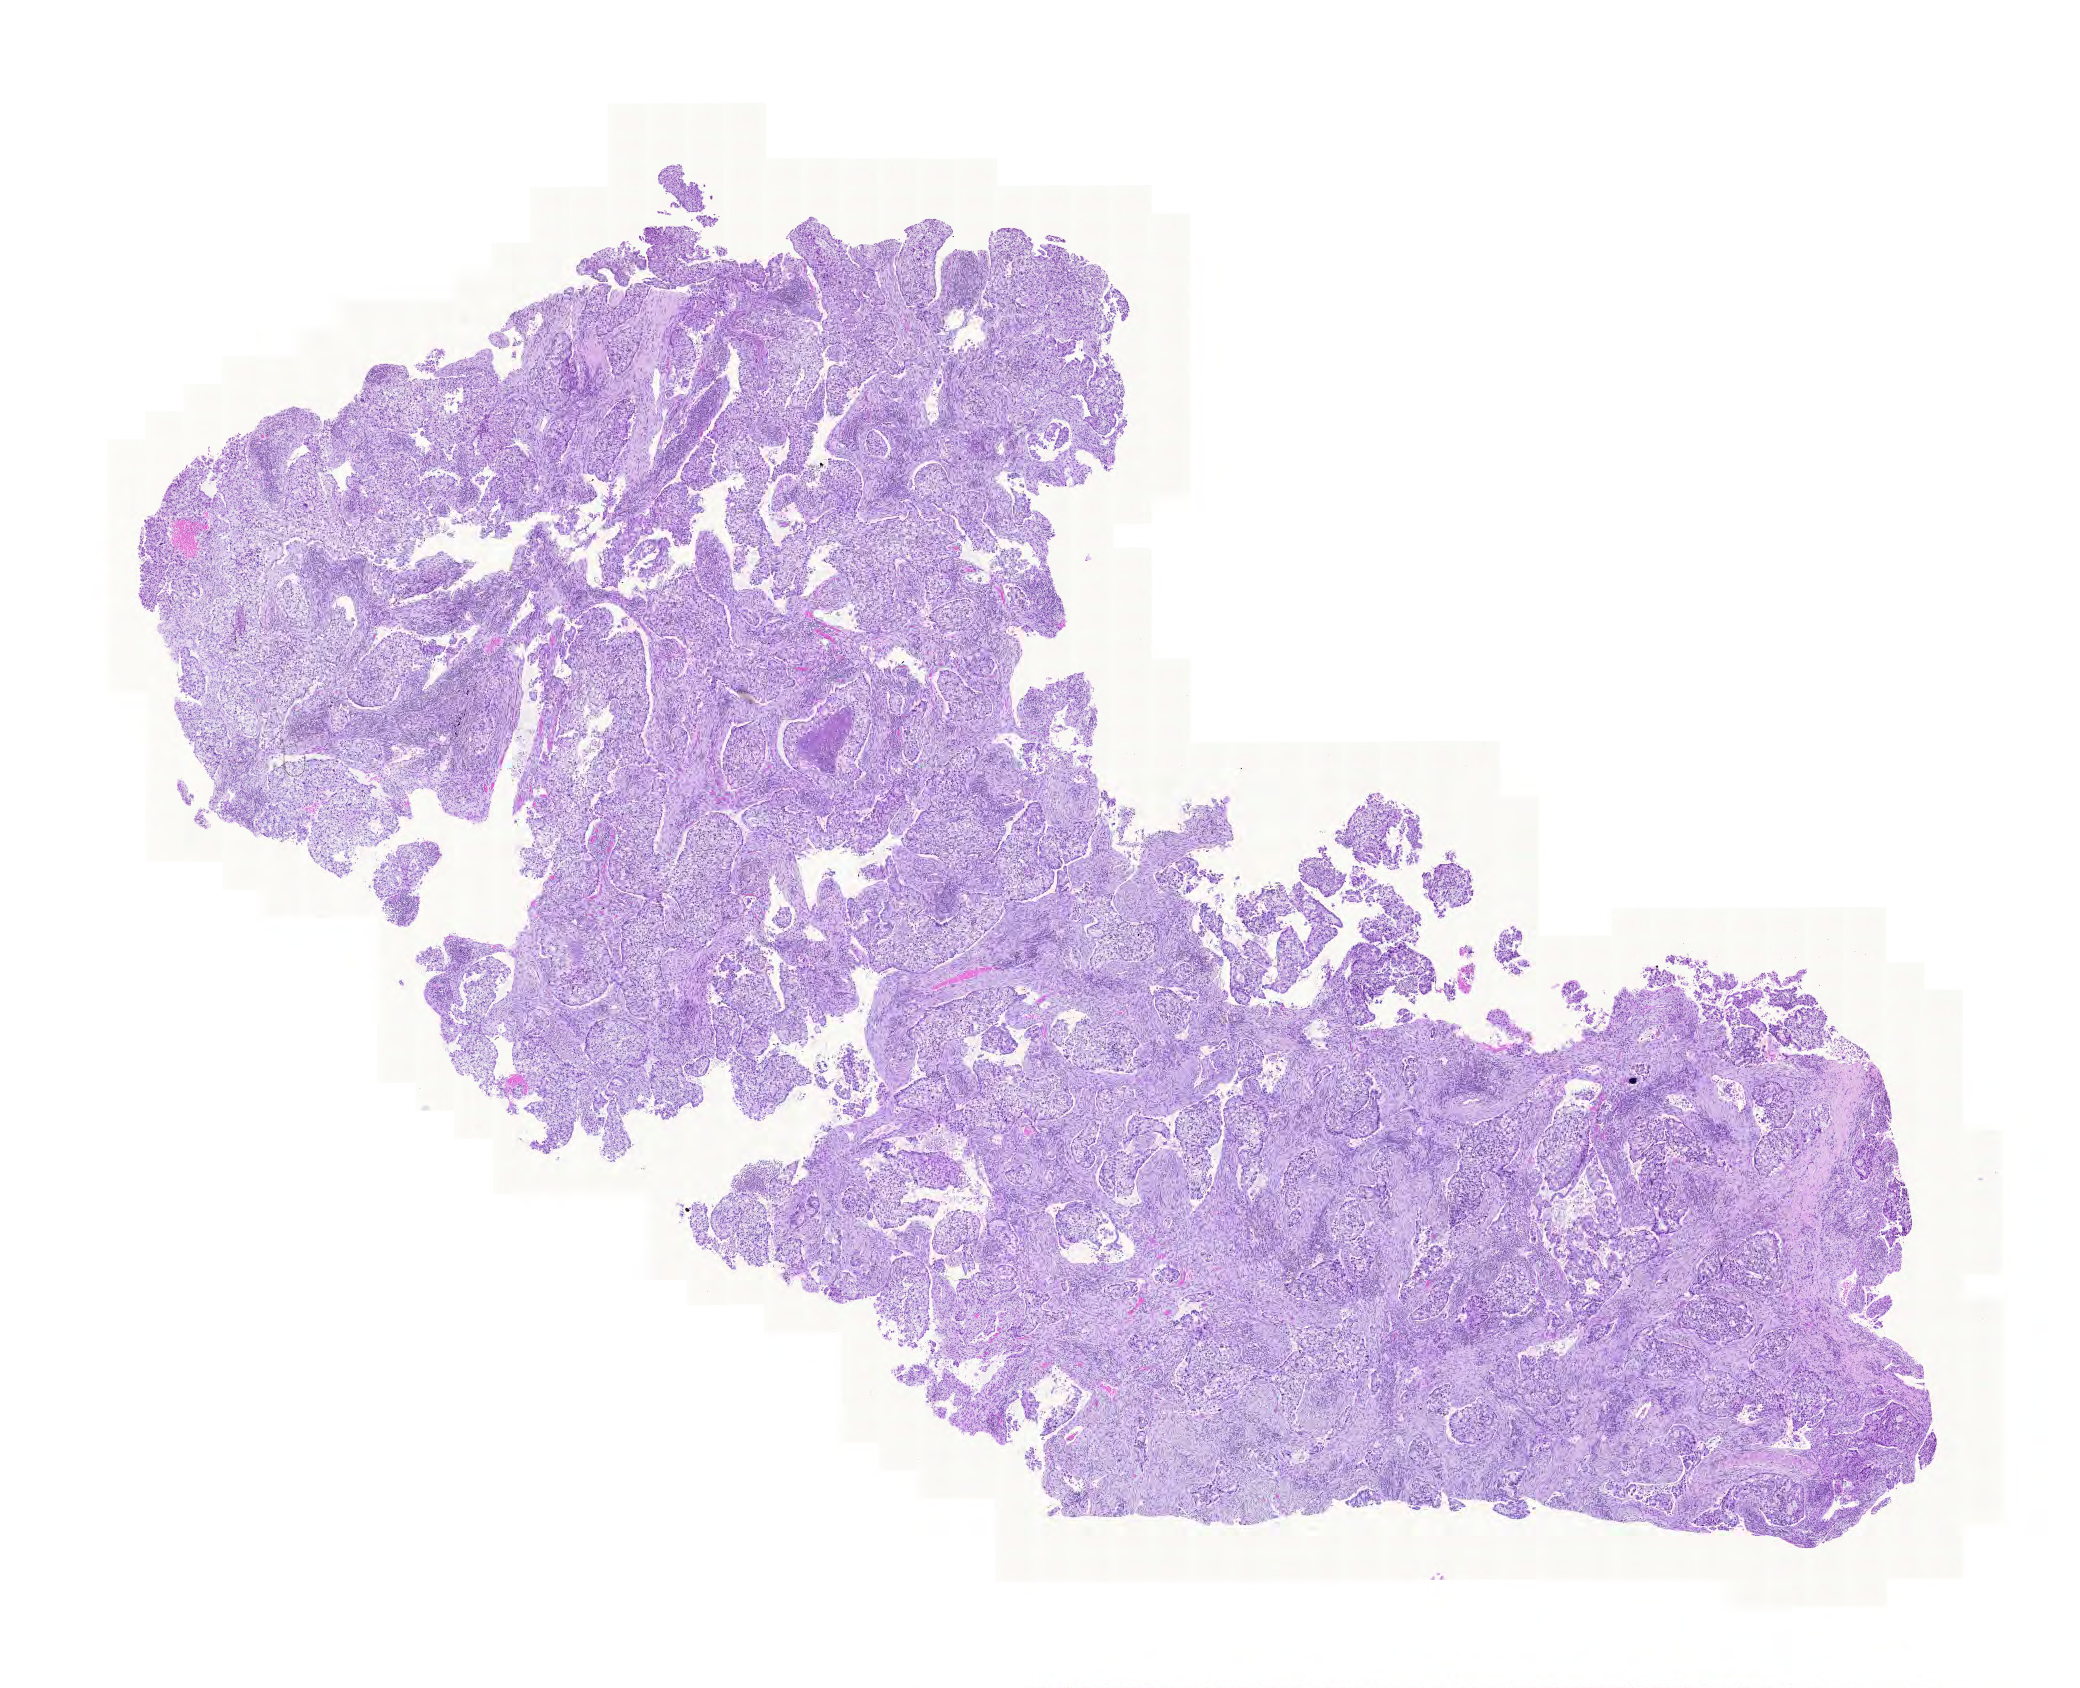
Whole-slide histology image, H&E-stained — a low-resolution overview of the entire scanned area, about 15.5 x 12.6 mm (from a 20x scan); FFPE section; lung, primary tumour sample. Female patient; age at initial diagnosis 51 years.
- TNM: T2 N0 M0
- pathologic diagnosis: Adenocarcinoma with mixed subtypes (upper lobe, lung)
- AJCC pathologic stage: IB (6th edition)
- laterality: right